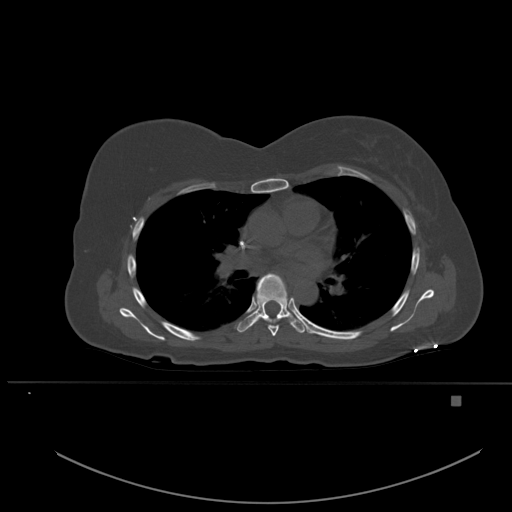
CT including the spine, one axial slice. Position 356 of 651 along the scan axis. Bone window (W 1800 / L 400 HU). 512 × 512 image matrix, field of view 443 × 443 mm. Female patient, age 49 years. From the clinical record (not read from this slice): primary cancer: breast.
Structures marked on this image (semi-automatically segmented with operator editing):
- T5 vertebra: box from (x=268, y=325) to (x=279, y=337) px
- T6 vertebra: (x=237, y=273)–(x=305, y=333)